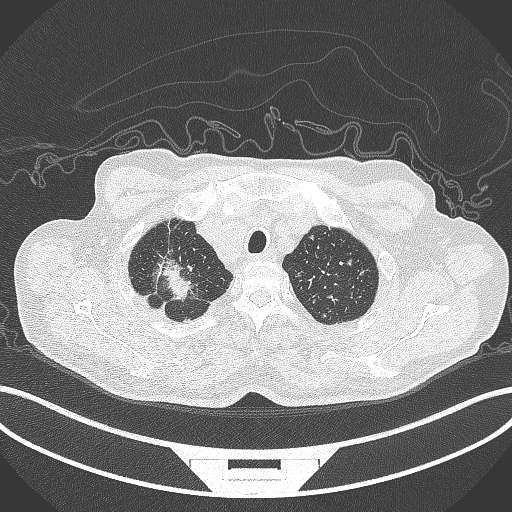
Chest CT, one axial slice. Slice 339 of 407 in the series (ordered by position). Lung window (W 1500 / L -600 HU). 512 × 512 image matrix. Patient: male, 69 years. Case-level facts recorded for this patient, not image findings: clinical TNM (as recorded): T1c N1 M1.
Structures marked on this image (rectangle marked by the reading radiologist):
- lung tumour (recorded histology: adenocarcinoma): bounding box [x1, y1, x2, y2] px = [148, 251, 201, 307]